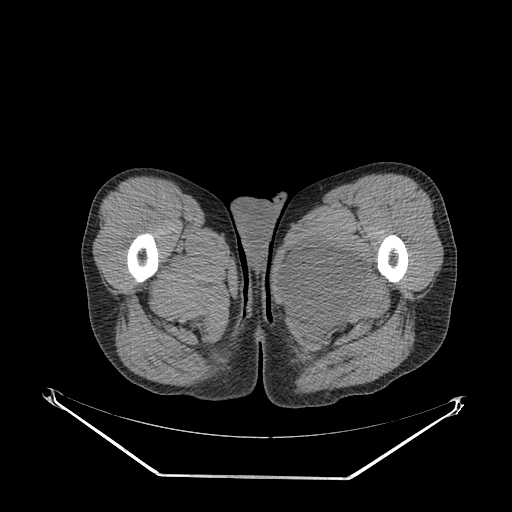
CT of an extremity soft-tissue mass (from a PET/CT study), one axial slice. Position 37 of 267 along the scan axis. Reconstruction kernel SOFT. Soft-tissue window (W 400 / L 40 HU). 3.75 mm slice thickness. 512 × 512 image matrix, field of view 500 × 500 mm. Male patient. Case-level facts recorded for this patient, not image findings: histological type: pleiomorphic liposarcoma; grade: high; site of the primary tumour: left thigh.
Annotated regions visible in this slice (expert contour drawn on MRI and transferred to this co-registered scan by the dataset authors):
- gross tumour volume including surrounding oedema: bounding box <285,237,366,328> (left, top, right, bottom; pixels)
- gross tumour volume (mass): <285,240,366,316>